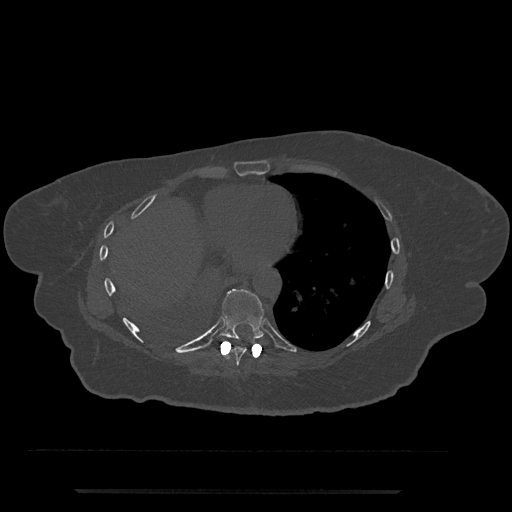
CT including the spine, one axial slice; slice 360 of 797 in the series (ordered by position); reconstruction kernel Br40s/3; 120 kVp; bone window (W 1800 / L 400 HU); 0.5 mm slice thickness; 512 × 512 image matrix, field of view 440 × 440 mm. Female patient, age 51 years. Case-level facts recorded for this patient, not image findings: primary cancer: neuro.
Structures marked on this image (semi-automatic segmentation, software-assisted and operator-edited):
- T8 vertebra: bounding box (x1, y1, x2, y2) in pixels: (229, 347, 247, 366)
- T9 vertebra: (212, 289, 264, 342)